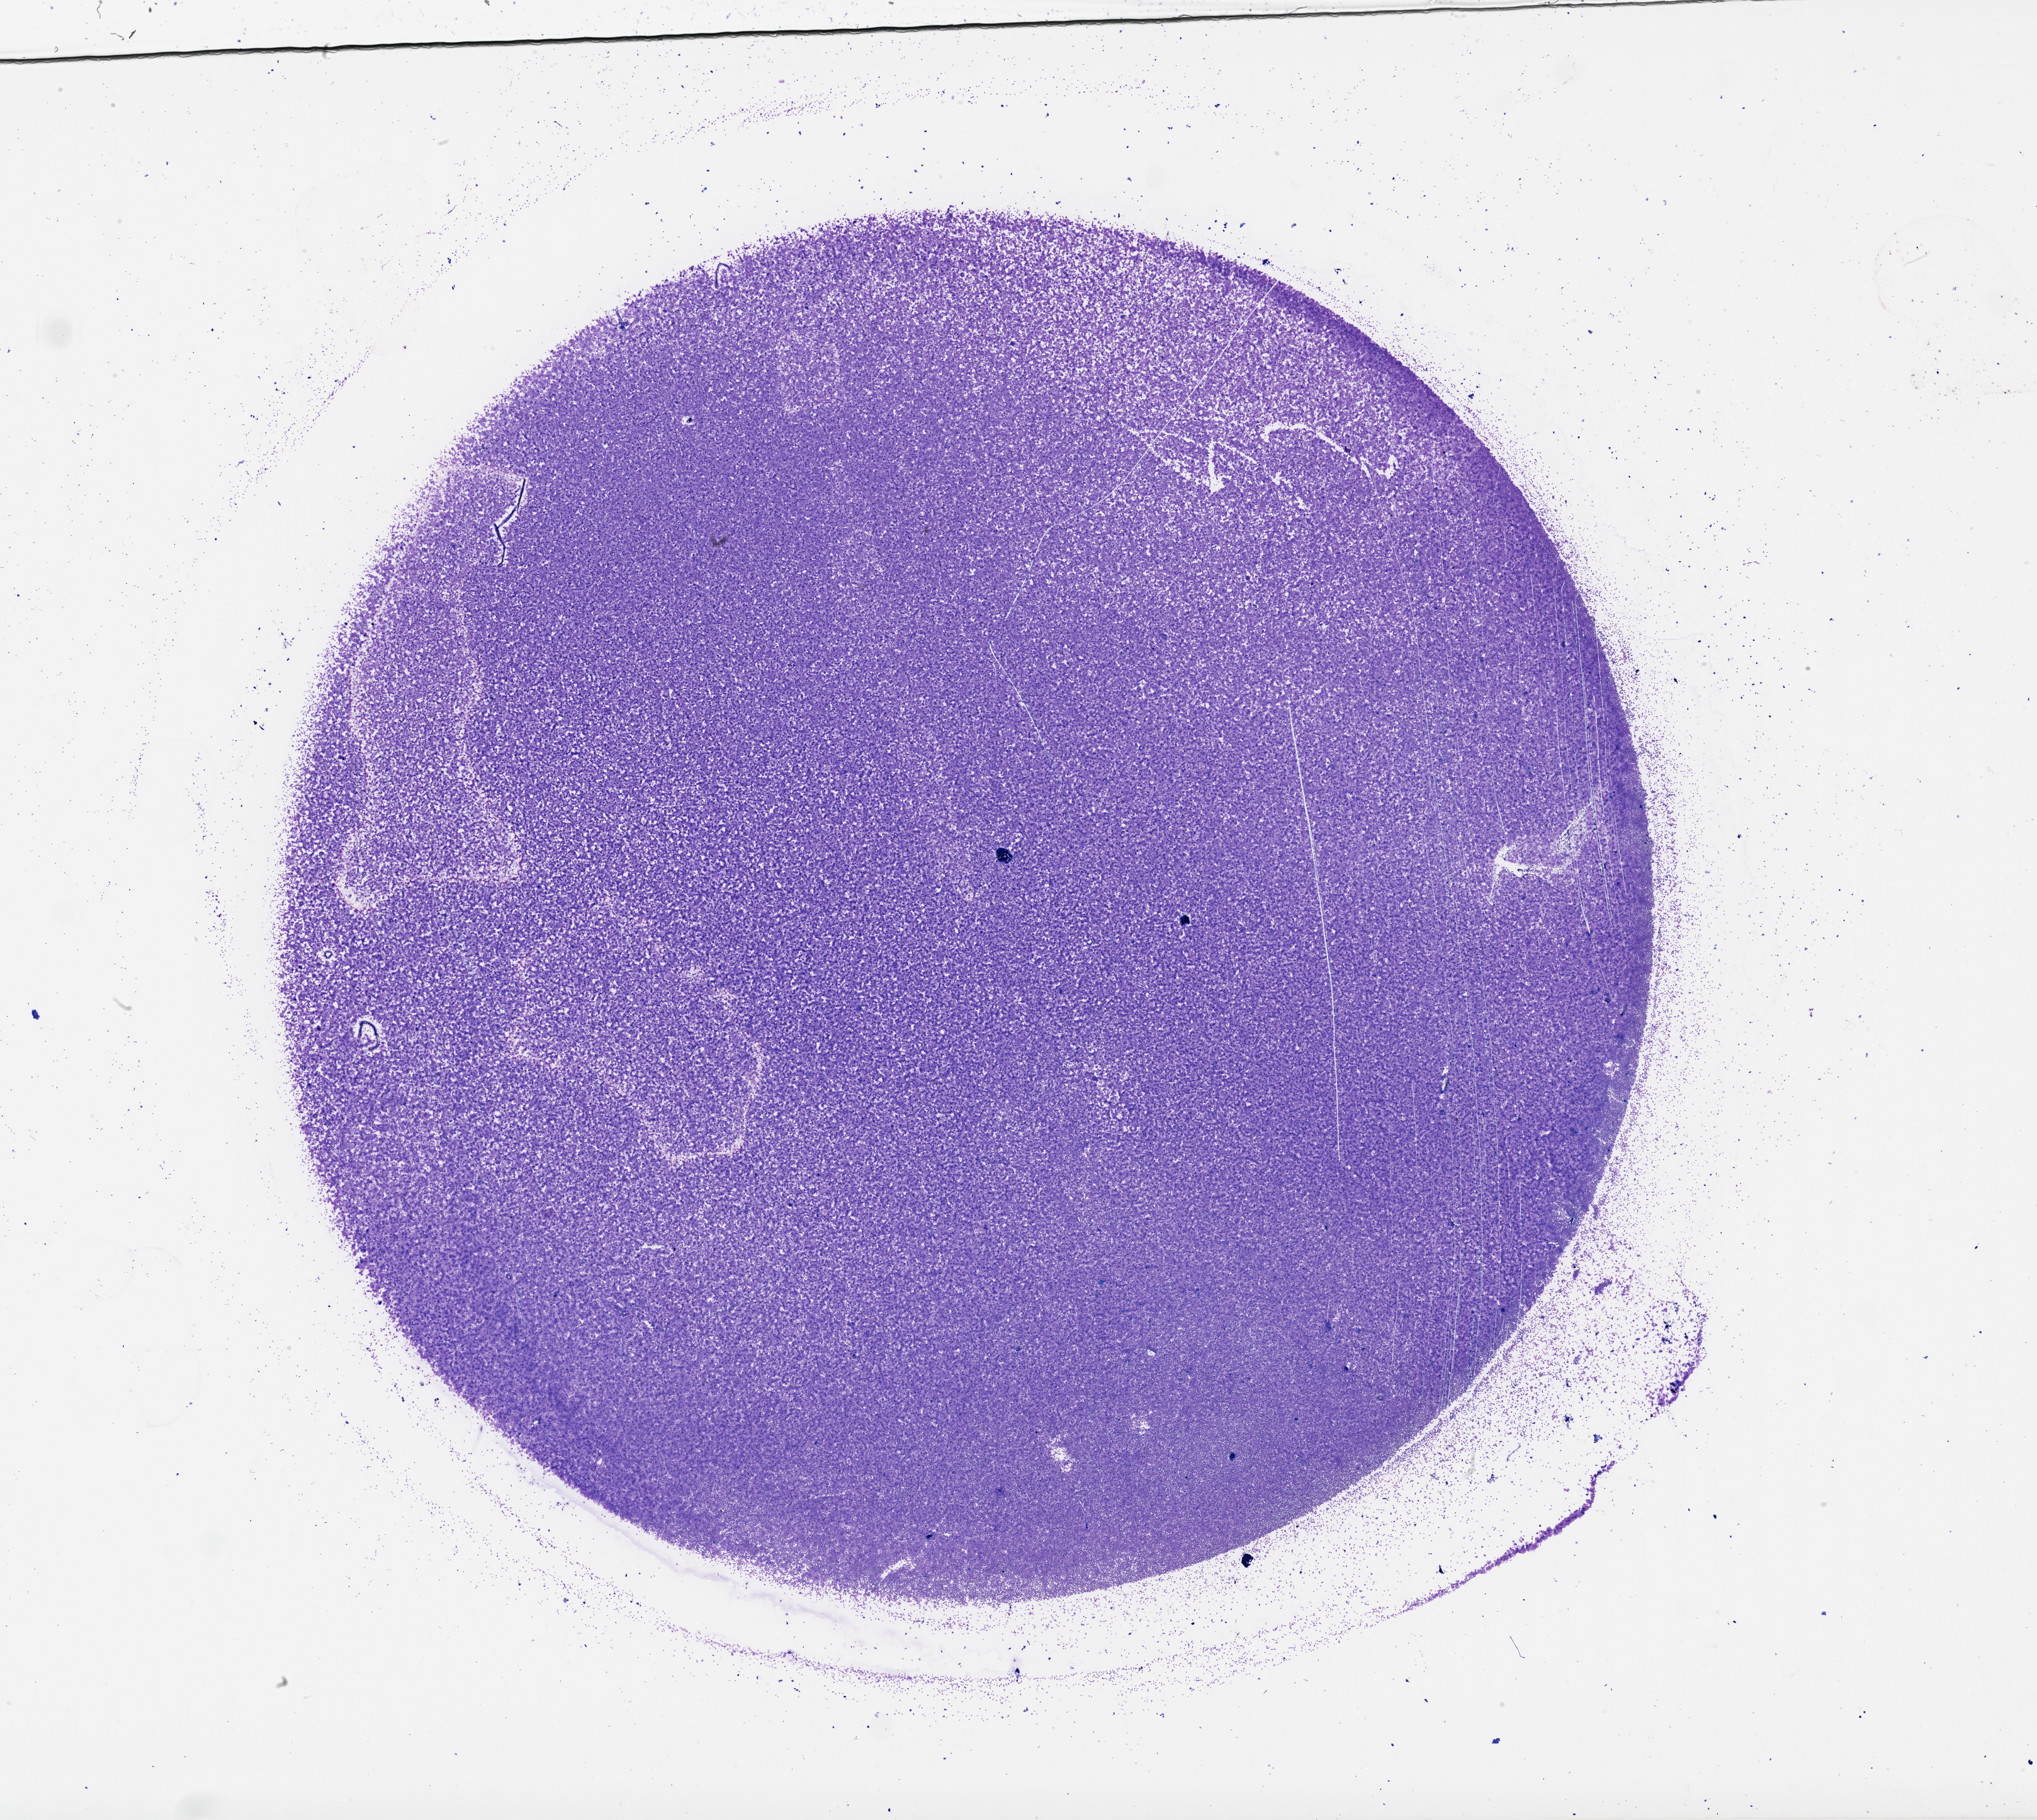
Whole-slide histology image, H&E — whole scanned area (about 26.1 x 23.3 mm, acquisition: 40x scan) shown as a low-resolution overview, bone marrow (leukaemic) sample. 45-year-old female patient. Blasts: 80%.
Diagnosis: Acute Myeloid Leukemia. FAB classification: M3.